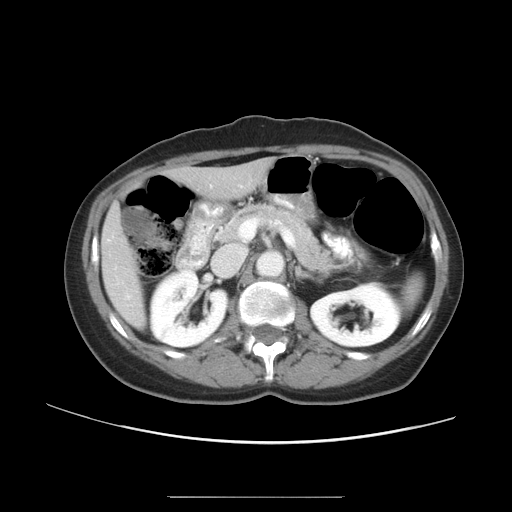
Contrast-enhanced abdominal CT, one axial slice; 120 kVp; intravenous contrast given; soft-tissue window (W 400 / L 40 HU); 5 mm slice thickness; 512 × 512 image matrix. Female patient, age 58 years. From the clinical record (not read from this slice): diagnosis: colorectal cancer liver metastases, imaged before liver resection; multiple liver metastases: yes; largest metastasis: 7.3 cm; disease in both lobes: yes.
Structures marked on this image (expert manual segmentation):
- liver: bounding box (x1, y1, x2, y2) in pixels: (103, 162, 268, 326)
- planned liver remnant (the part of the liver to remain after resection): (179, 162, 269, 198)